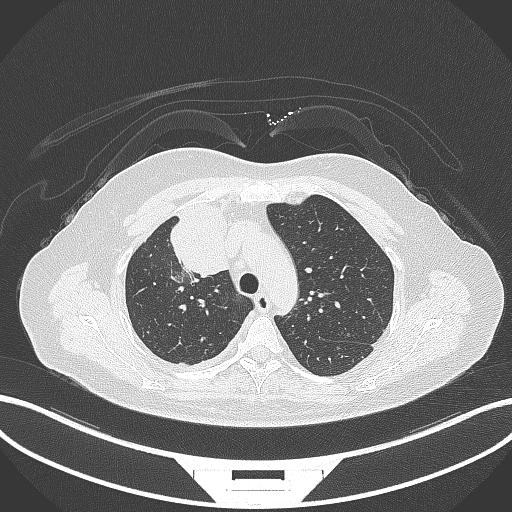
Chest CT, one axial slice. Slice 221 of 305 in the series (ordered by position). Reconstruction kernel B70f. 120 kVp. Lung window (W 1500 / L -600 HU). 512 × 512 image matrix, field of view 400 × 400 mm. Patient: female, 52 years. From the clinical record (not read from this slice): clinical TNM (as recorded): T3 N1 M1.
Outlined on this slice (bounding box drawn by a radiologist):
- lung tumour (recorded histology: adenocarcinoma): bounding box <169,203,236,278> (left, top, right, bottom; pixels)